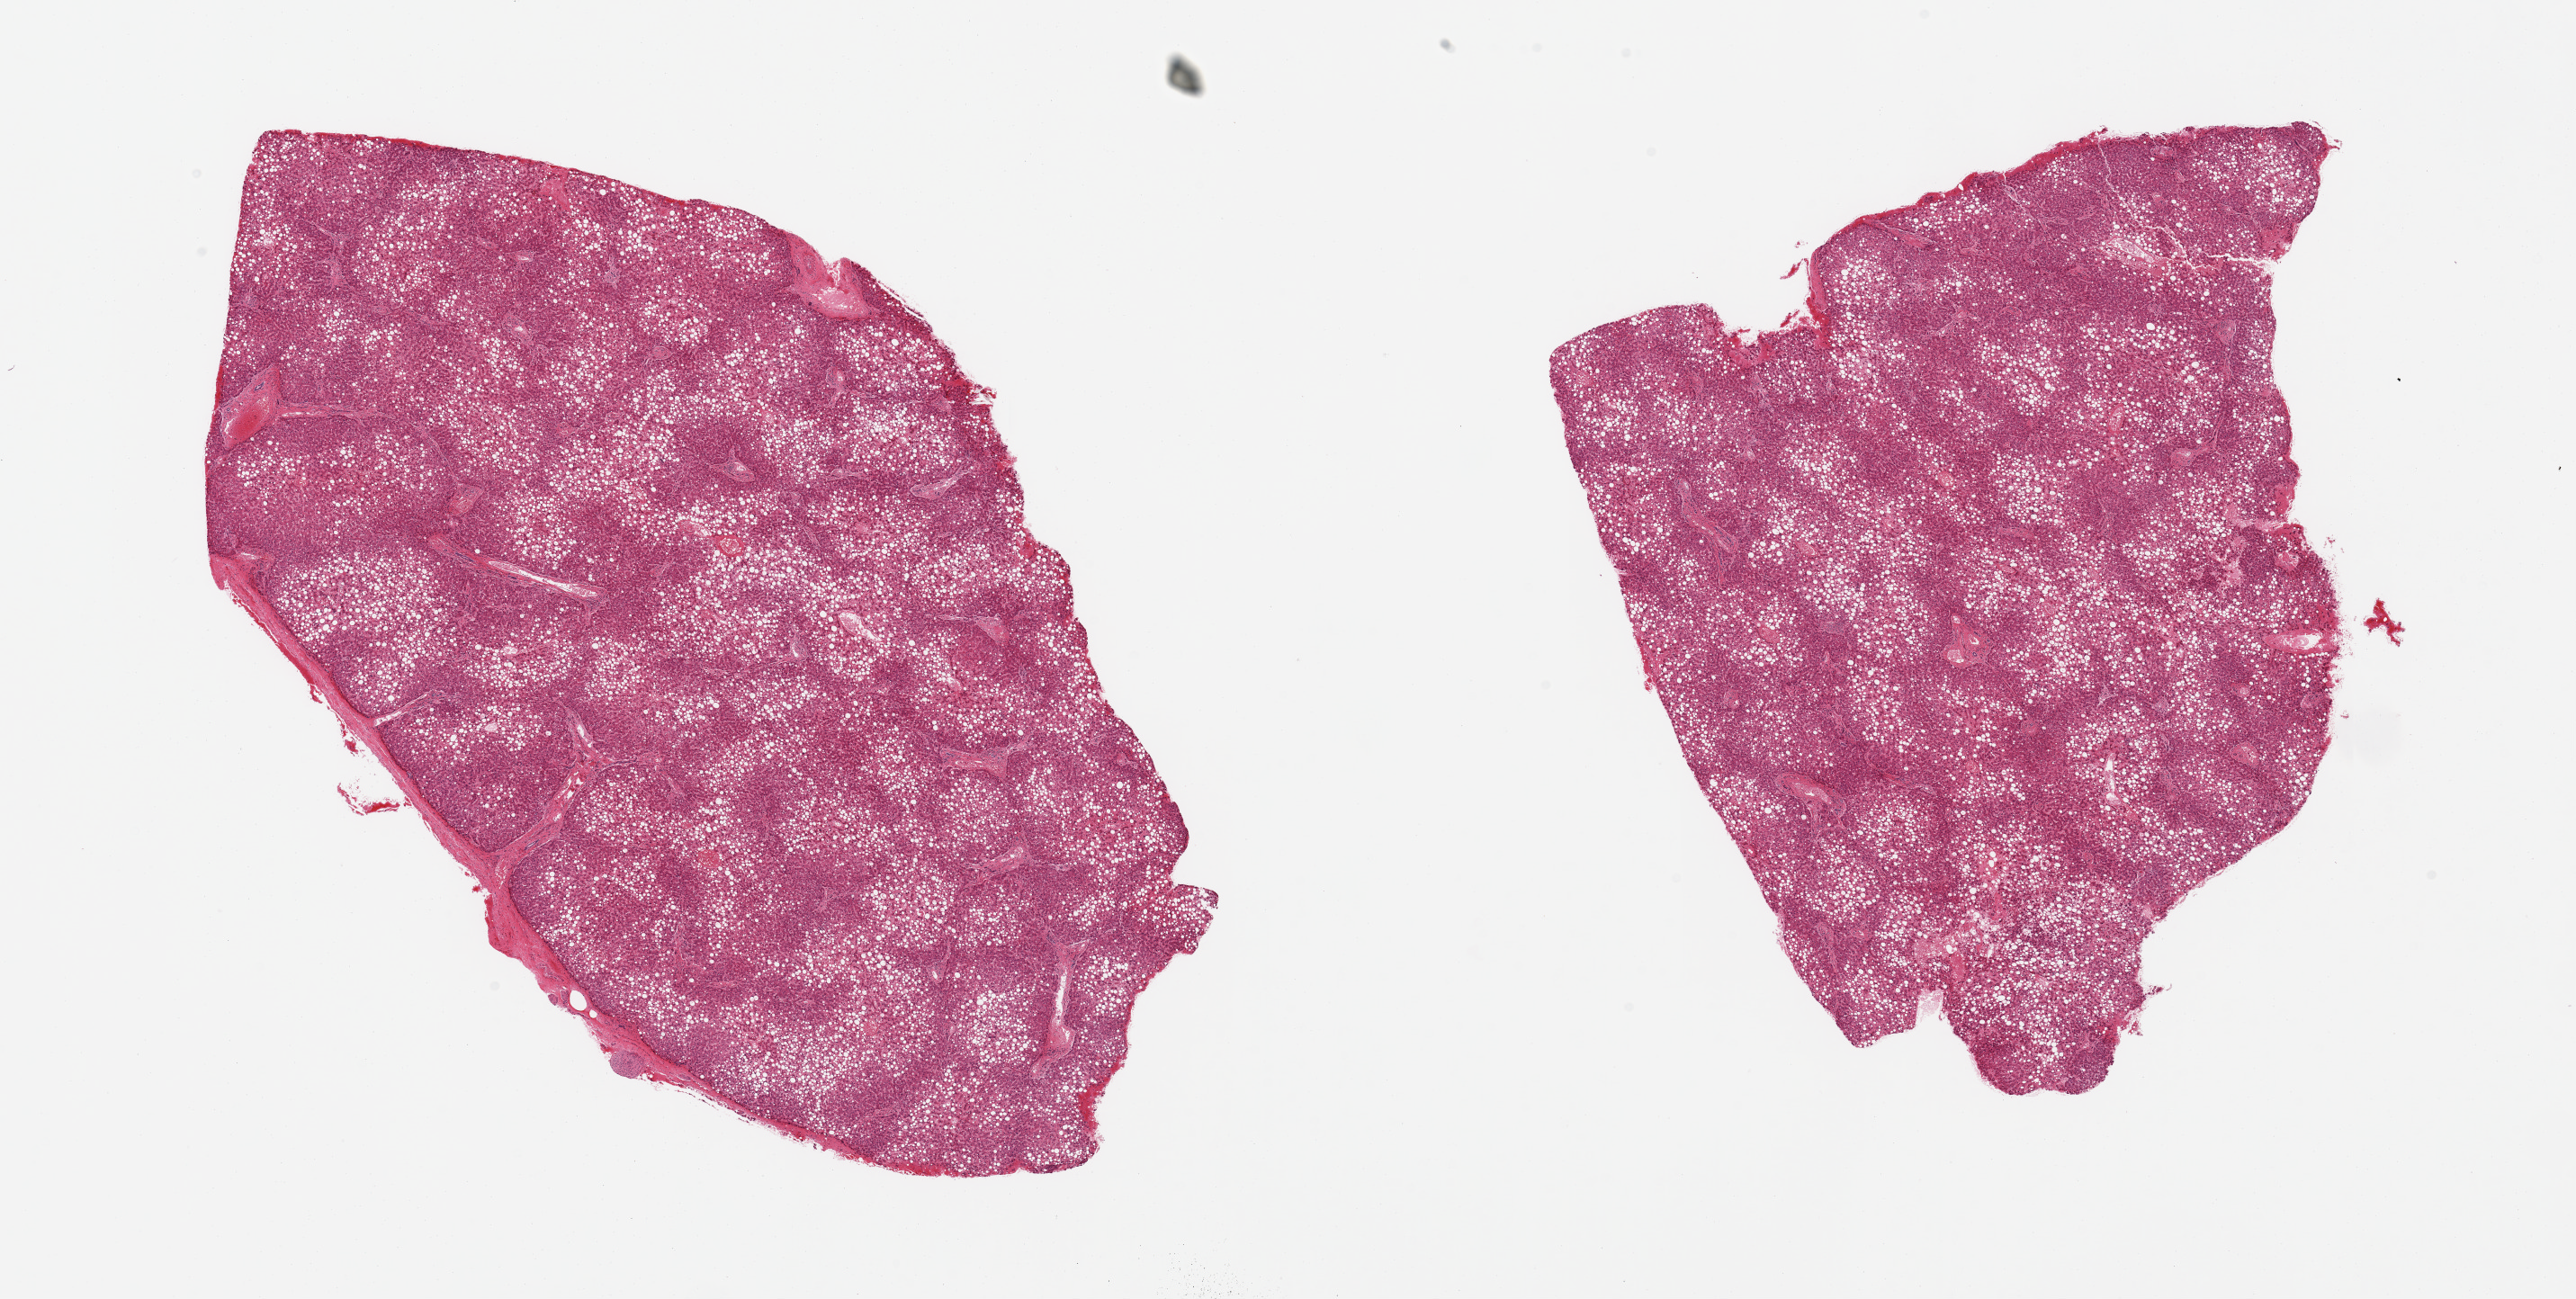
Whole-slide image, H&E stain, brightfield — whole scanned area (about 22.6 x 11.4 mm) shown as a low-resolution overview; PAXgene-fixed, paraffin-embedded tissue; target tissue: liver; tissue donor sample. Donor sex: male.
Pathologist's review note for this sample: 2 pieces; diffuse and marked steatosis (micro and macrovesicular fat).